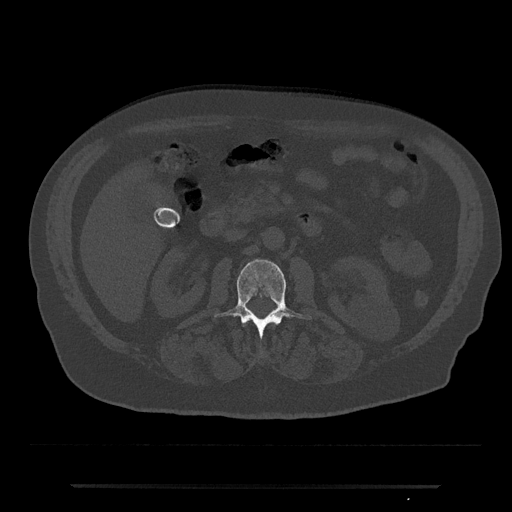
CT including the spine, one axial slice. Slice 474 of 797 in the series (ordered by position). Reconstruction kernel Br40s/3. 120 kVp. Bone window (W 1800 / L 400 HU). 512 × 512 image matrix, field of view 434 × 434 mm. Male patient, age 80 years. From the clinical record (not read from this slice): primary cancer: prostate.
Annotated regions visible in this slice (semi-automatically segmented with operator editing):
- L2 vertebra: bounding box (x1, y1, x2, y2) in pixels: (214, 259, 312, 339)